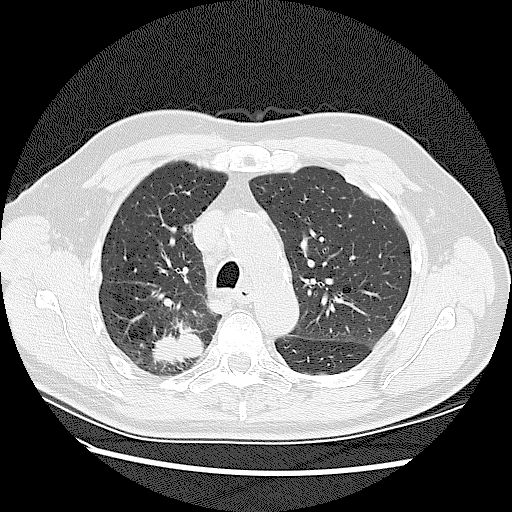
Low-dose screening chest CT, one axial slice; slice 90 of 128 in the series (ordered by position); reconstruction kernel LUNG; 120 kVp; lung window (W 1500 / L -600 HU); 2.5 mm slice thickness; 512 × 512 image matrix.
Annotated regions visible in this slice (outlined manually by an expert reader):
- lesion 2 (tumor, upper lobe of right lung): bounding box <154,333,203,361> (left, top, right, bottom; pixels)